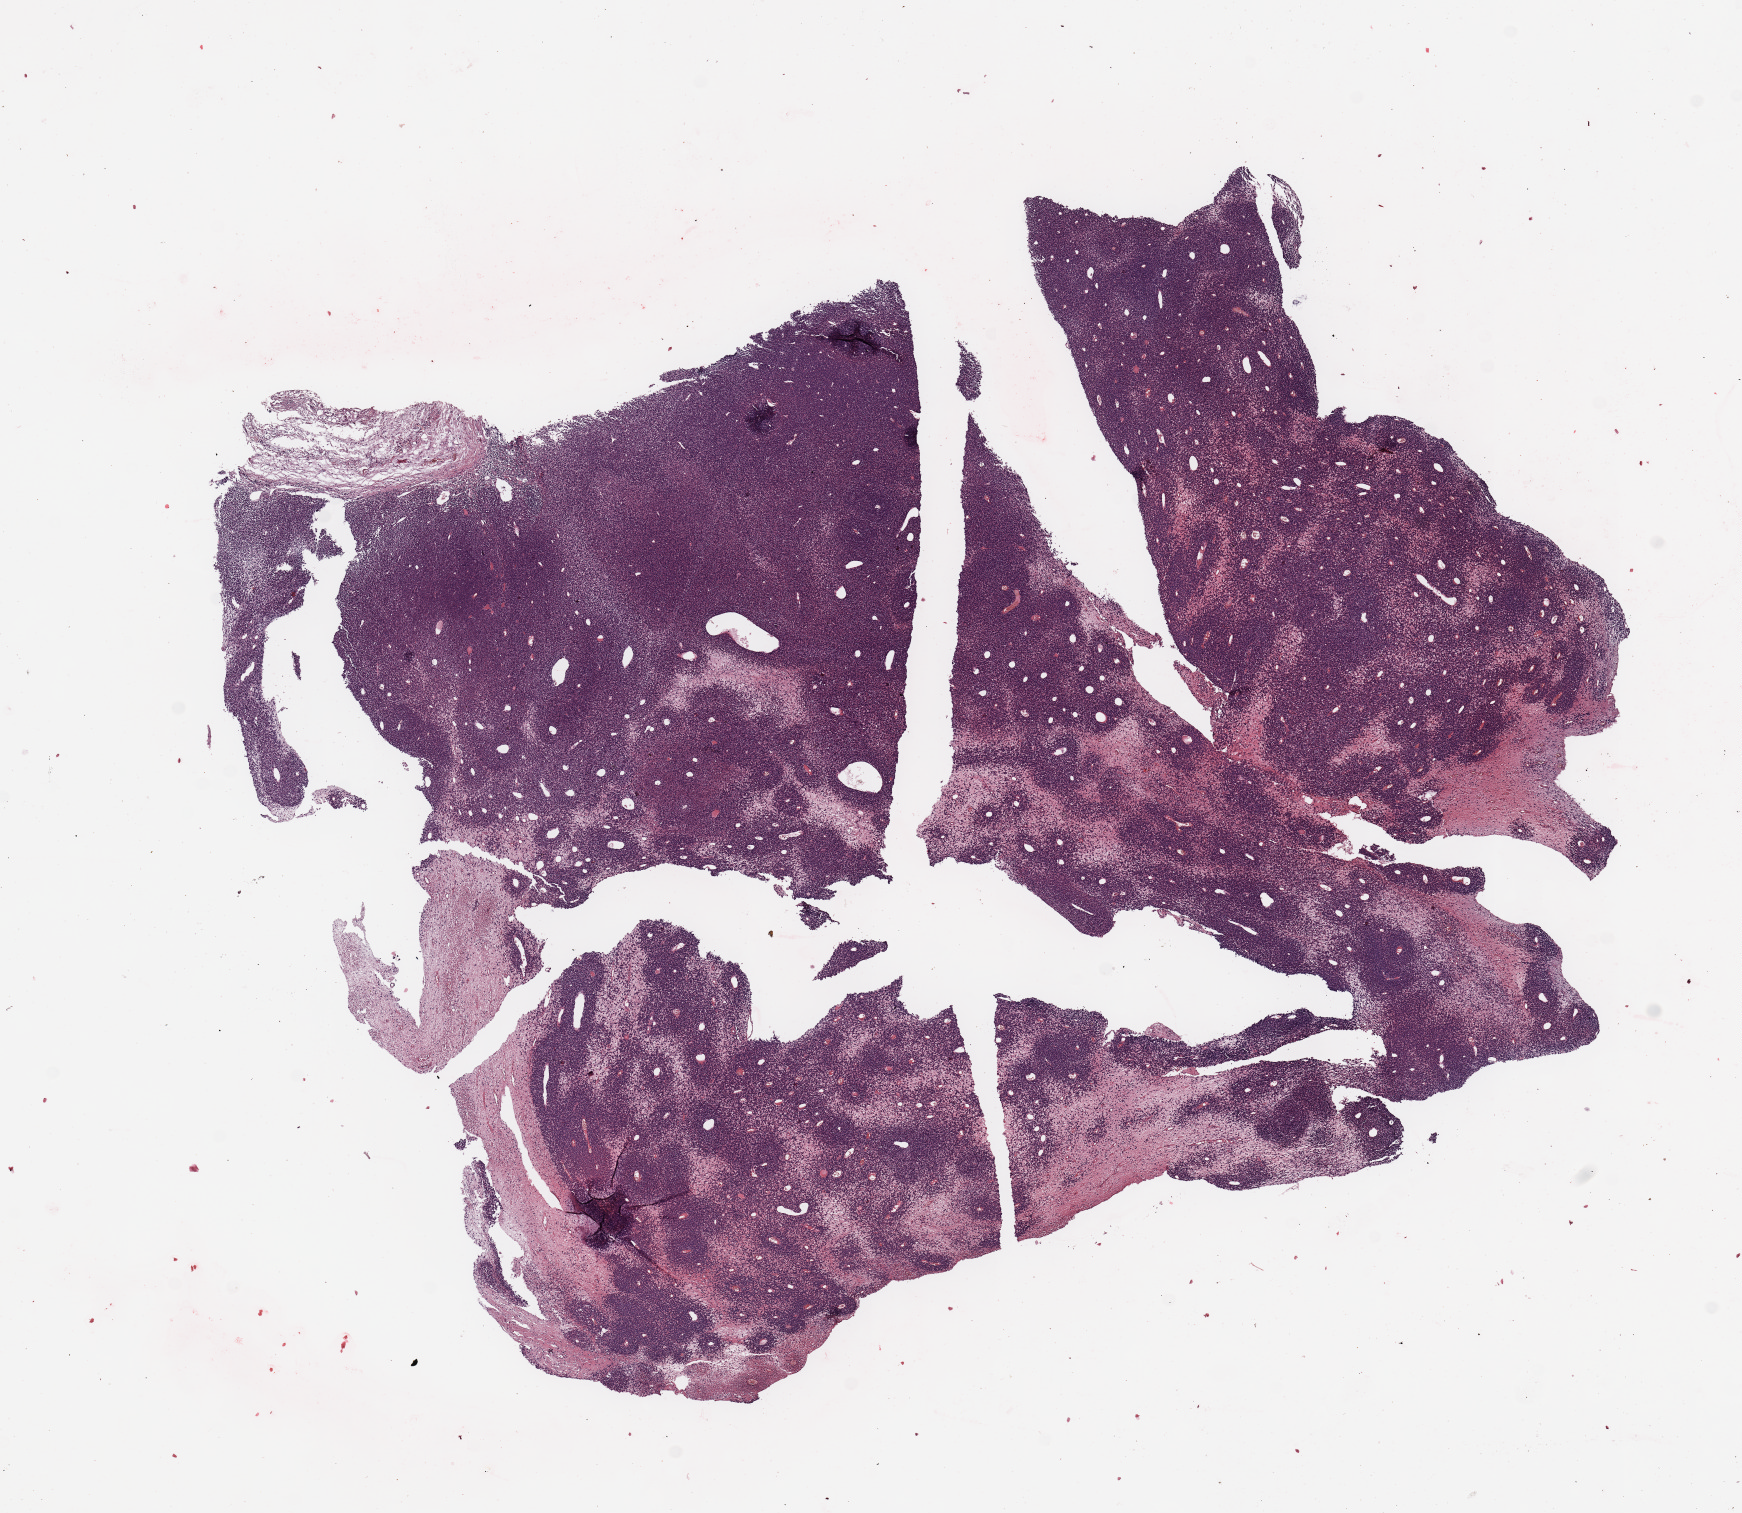
Hematoxylin and eosin (H&E) stained whole-slide image, shown as a low-resolution overview of the whole scanned area (about 13.8 x 12.0 mm, from a 20x scan); tumour tissue sample, sampled site: lymph node. 76-year-old female patient. Pathologist review of this section (percent, as recorded): tumour nuclei 98%, necrosis 0%.
This section: metastatic tumour tissue. Primary tumour site (as recorded): trunk. Patient diagnosis: Malignant melanoma, NOS.